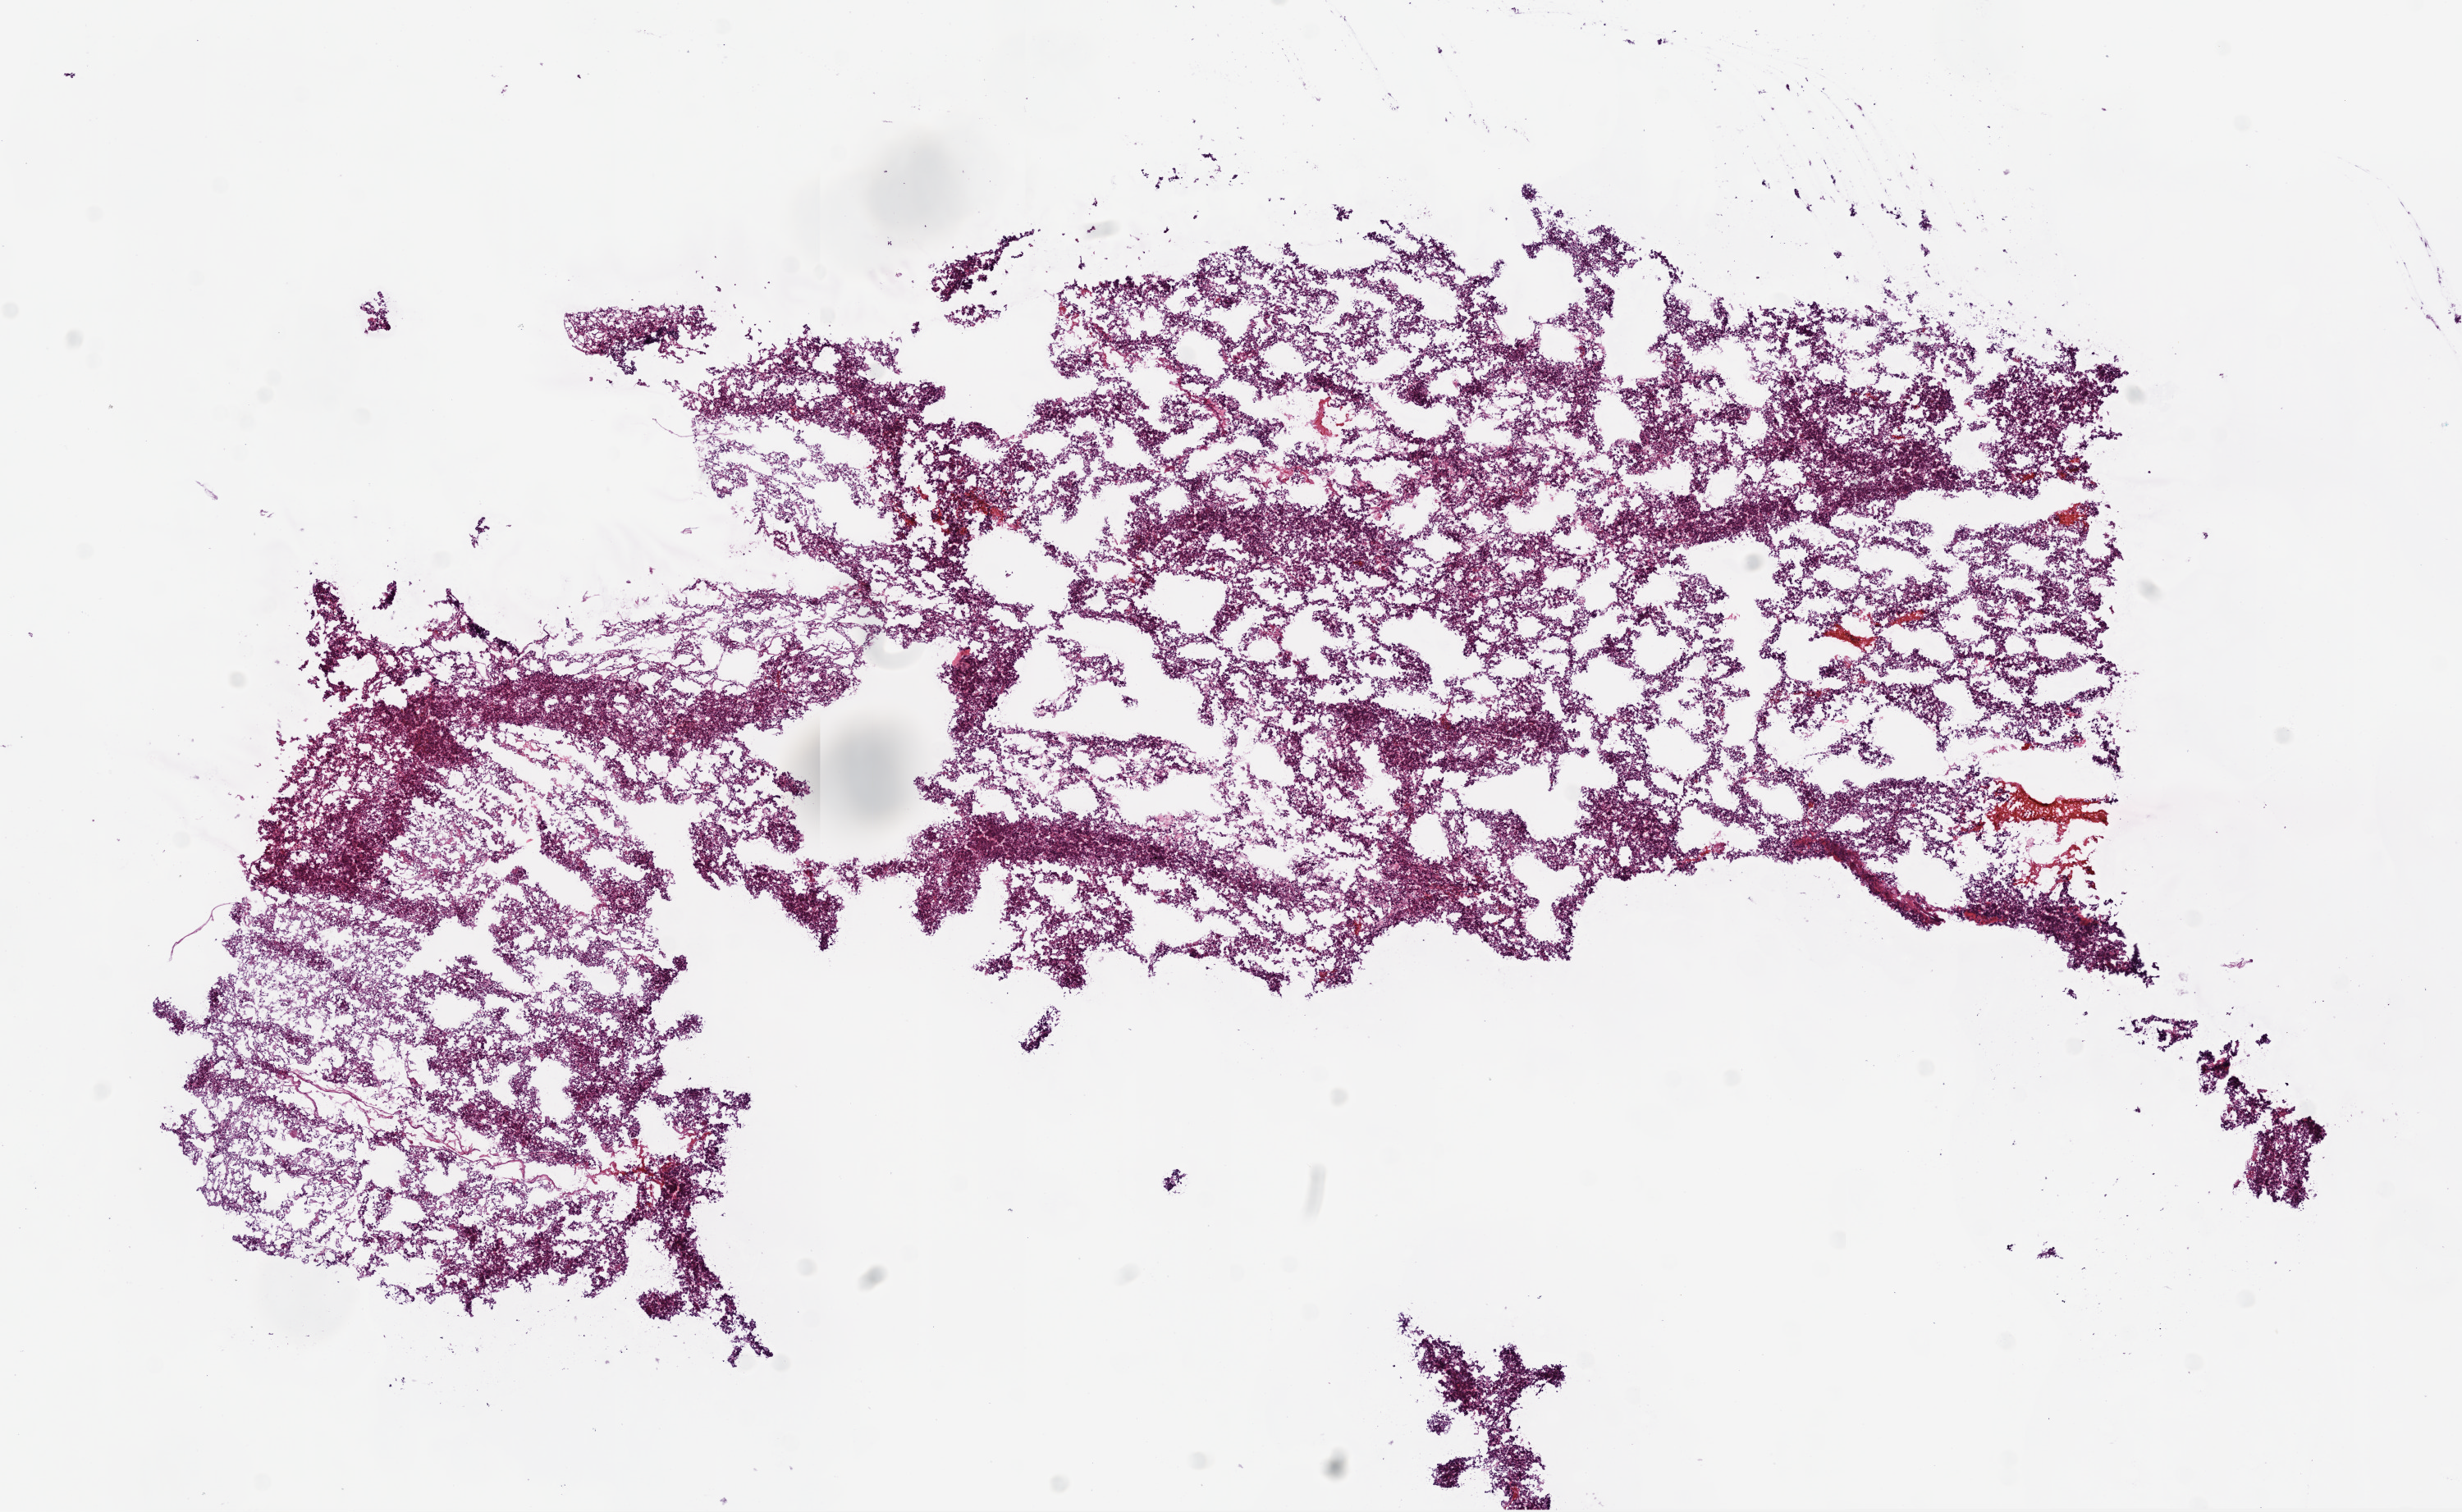
Whole-slide histology image, H&E, a low-resolution overview of the entire scanned area, about 12.0 x 7.4 mm (slide scanned at 20x); frozen section; sample: primary tumour, kidney. Female, age 80 years at initial diagnosis. Histologic grade: G2 (moderately differentiated). Slide review estimates, as recorded: tumour cells 92%, tumour nuclei 85%, normal cells 0%, stromal cells 5%, necrosis 3%.
AJCC pathologic stage: I. Pathologic diagnosis: Clear cell adenocarcinoma, NOS.